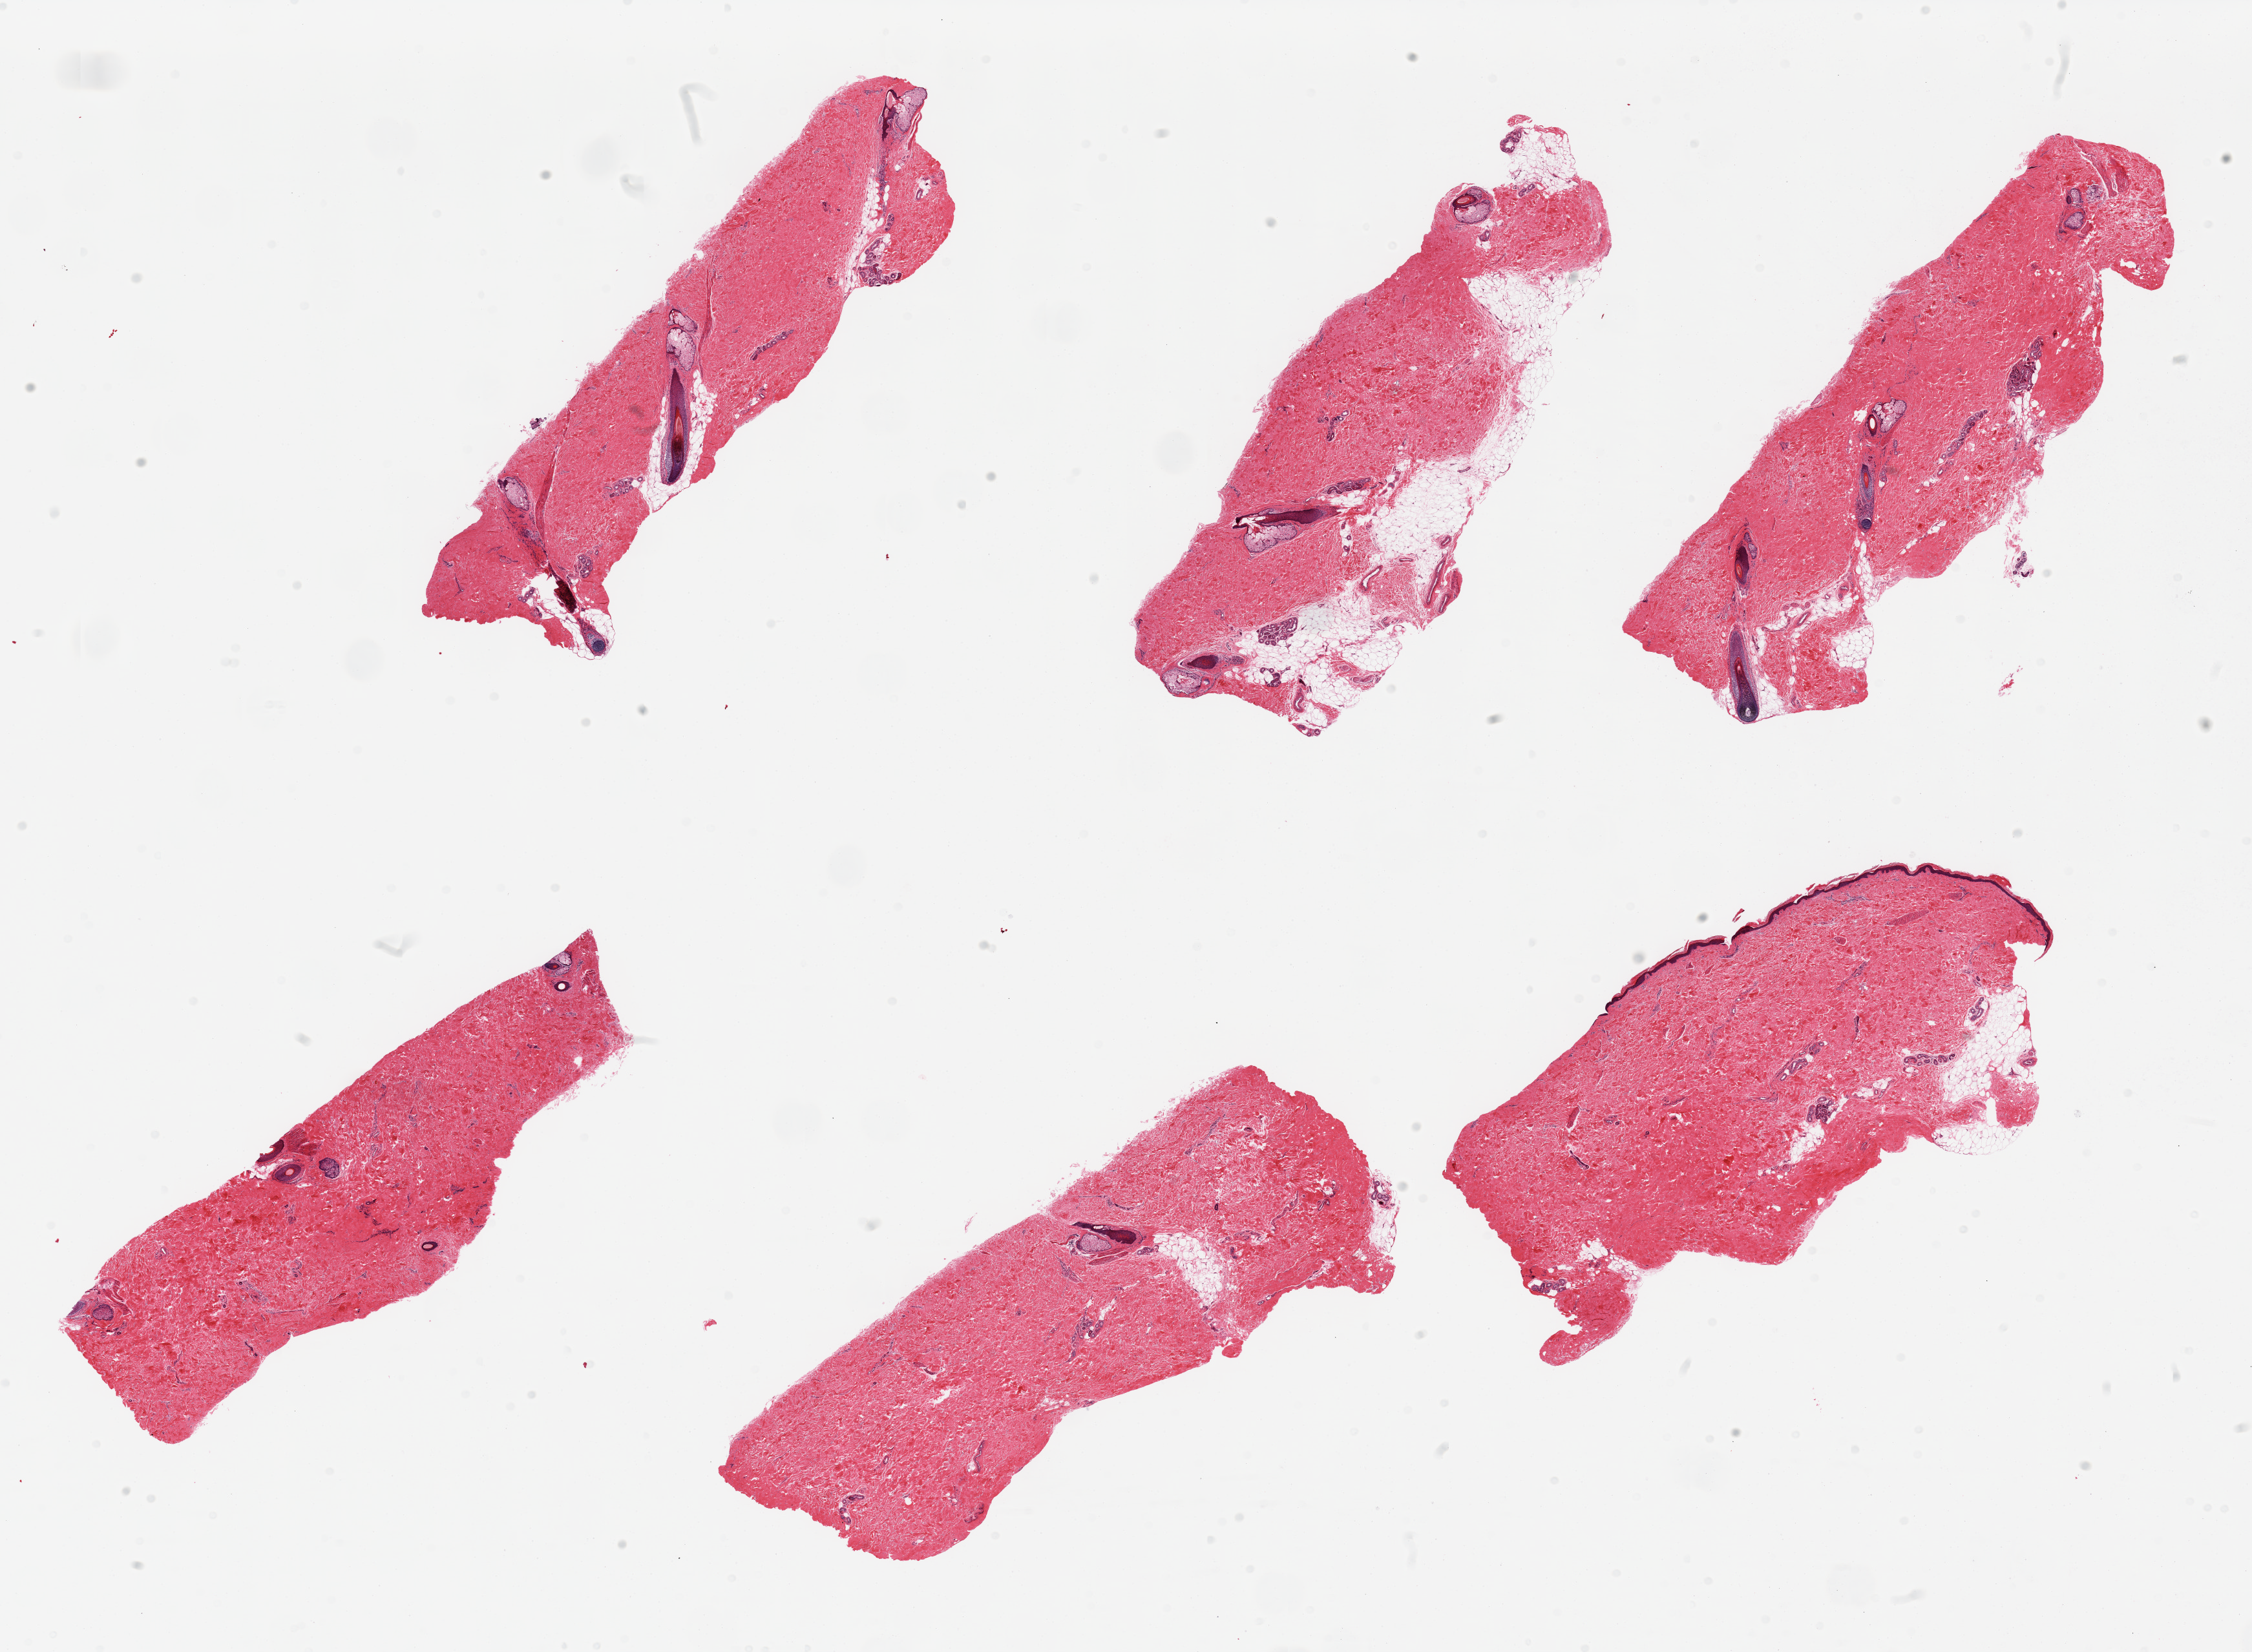
Whole-slide image, H&E stain — low-resolution overview of the scanned area, about 27.6 x 20.2 mm (acquisition: 20x scan). PAXgene-fixed, paraffin-embedded tissue. Section of skin of lower leg (target tissue). Donor tissue sample. Donor sex: male.
Review note (as recorded): 6 pieces, 5 of 6 do not show squamous epithelium (? embedding).